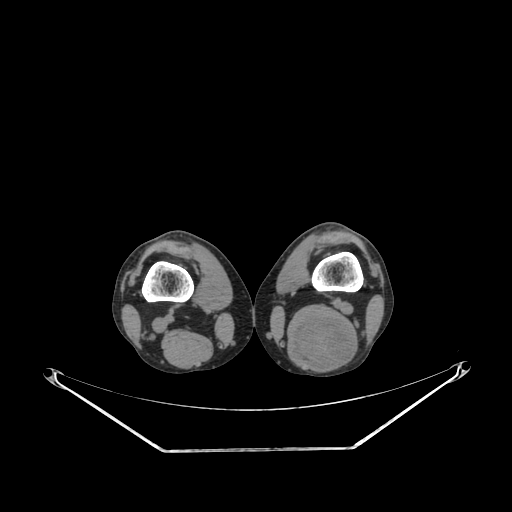
CT of an extremity soft-tissue mass (from a PET/CT study), one axial slice; slice 191 of 267 in the series (ordered by position); reconstruction kernel SOFT; soft-tissue window (W 400 / L 40 HU); 512 × 512 image matrix, field of view 500 × 500 mm. Male patient. Case-level facts recorded for this patient, not image findings: histological type: synovial sarcoma; site of the primary tumour: left poplietal fossa.
Annotated regions visible in this slice (expert contour drawn on MRI and transferred to this co-registered scan by the dataset authors):
- gross tumour volume (mass): bounding box <288,315,359,371> (left, top, right, bottom; pixels)